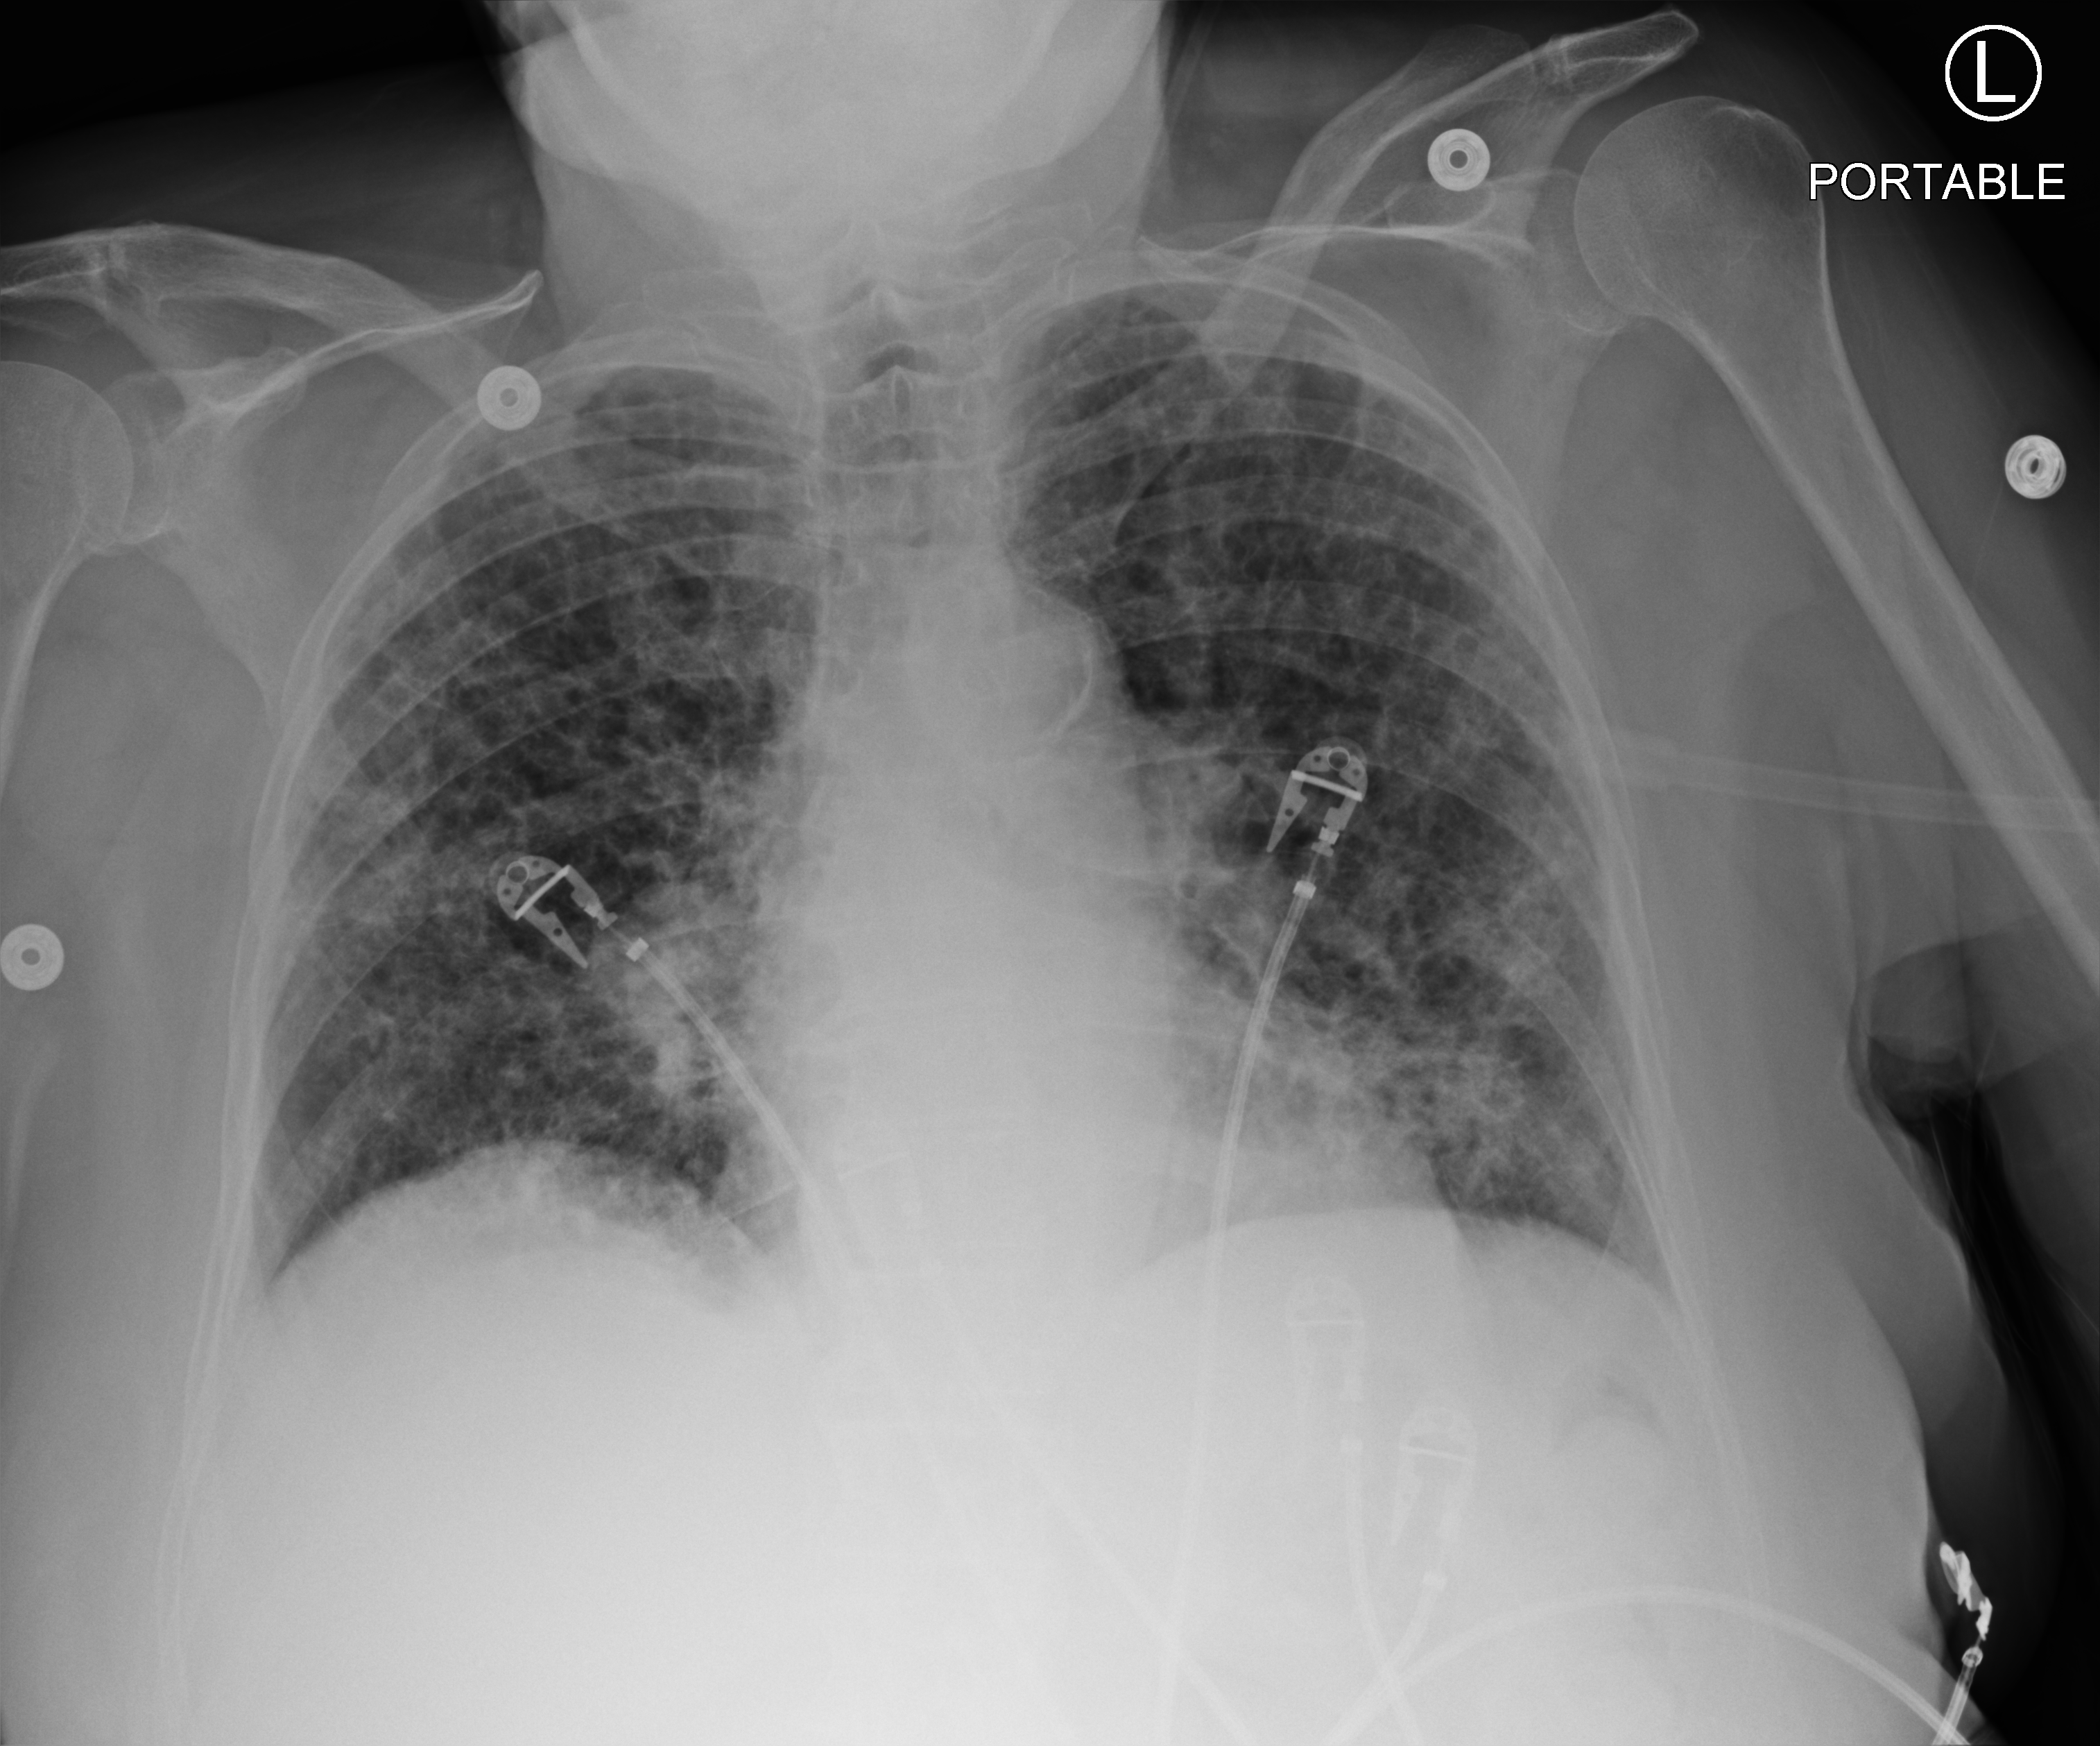
Bedside chest radiograph (computed radiography). Female patient hospitalised with COVID-19, age 75–90 years.
From the hospital-stay record, not from the radiograph (when in the stay this image was taken is not recorded): mechanically ventilated during this hospital stay: no; admitted to intensive care during this hospital stay: no; COPD (admission record): yes.